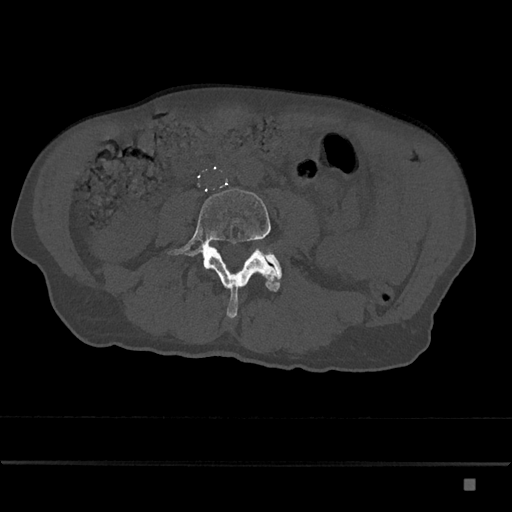
CT including the spine, one axial slice. Slice 334 of 797 in the series (ordered by position). Bone window (W 1800 / L 400 HU). 512 × 512 image matrix, field of view 390 × 390 mm. Patient: male, 72 years. From the clinical record (not read from this slice): primary cancer: prostate.
Annotated regions visible in this slice (semi-automatic segmentation, software-assisted and operator-edited):
- L4 vertebra: box from (x=167, y=189) to (x=282, y=319) px
- L5 vertebra: (x=267, y=254)–(x=282, y=275)